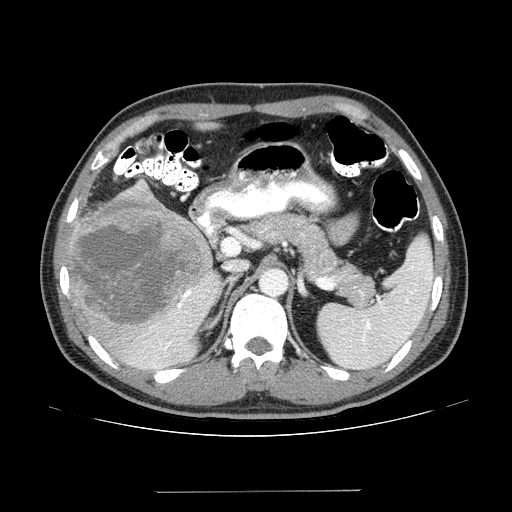
Contrast-enhanced abdominal CT (liver protocol), one axial slice. Slice 83 of 131 in the series (ordered by position). Reconstruction kernel STANDARD. One of 2 acquisitions stored at this slice position. Soft-tissue window (W 400 / L 40 HU). 512 × 512 image matrix, field of view 380 × 380 mm. From the clinical record (not read from this slice): diagnosis: hepatocellular carcinoma (patient treated with transarterial chemoembolisation; whether this scan precedes or follows treatment is not stated here); TNM stage (as recorded): Stage-I; Child-Pugh class: A; tumour differentiation: poorly differentiated; tumour nodularity: uninodular.
Outlined on this slice (semi-automatic segmentation, software-assisted and operator-edited):
- liver parenchyma outside the tumour (the mass and vessels are separate outlines, so this box may not span the whole liver): bounding box [x1, y1, x2, y2] px = [66, 180, 222, 370]
- mass: [68, 187, 211, 329]
- liver vessels: [143, 289, 209, 368]